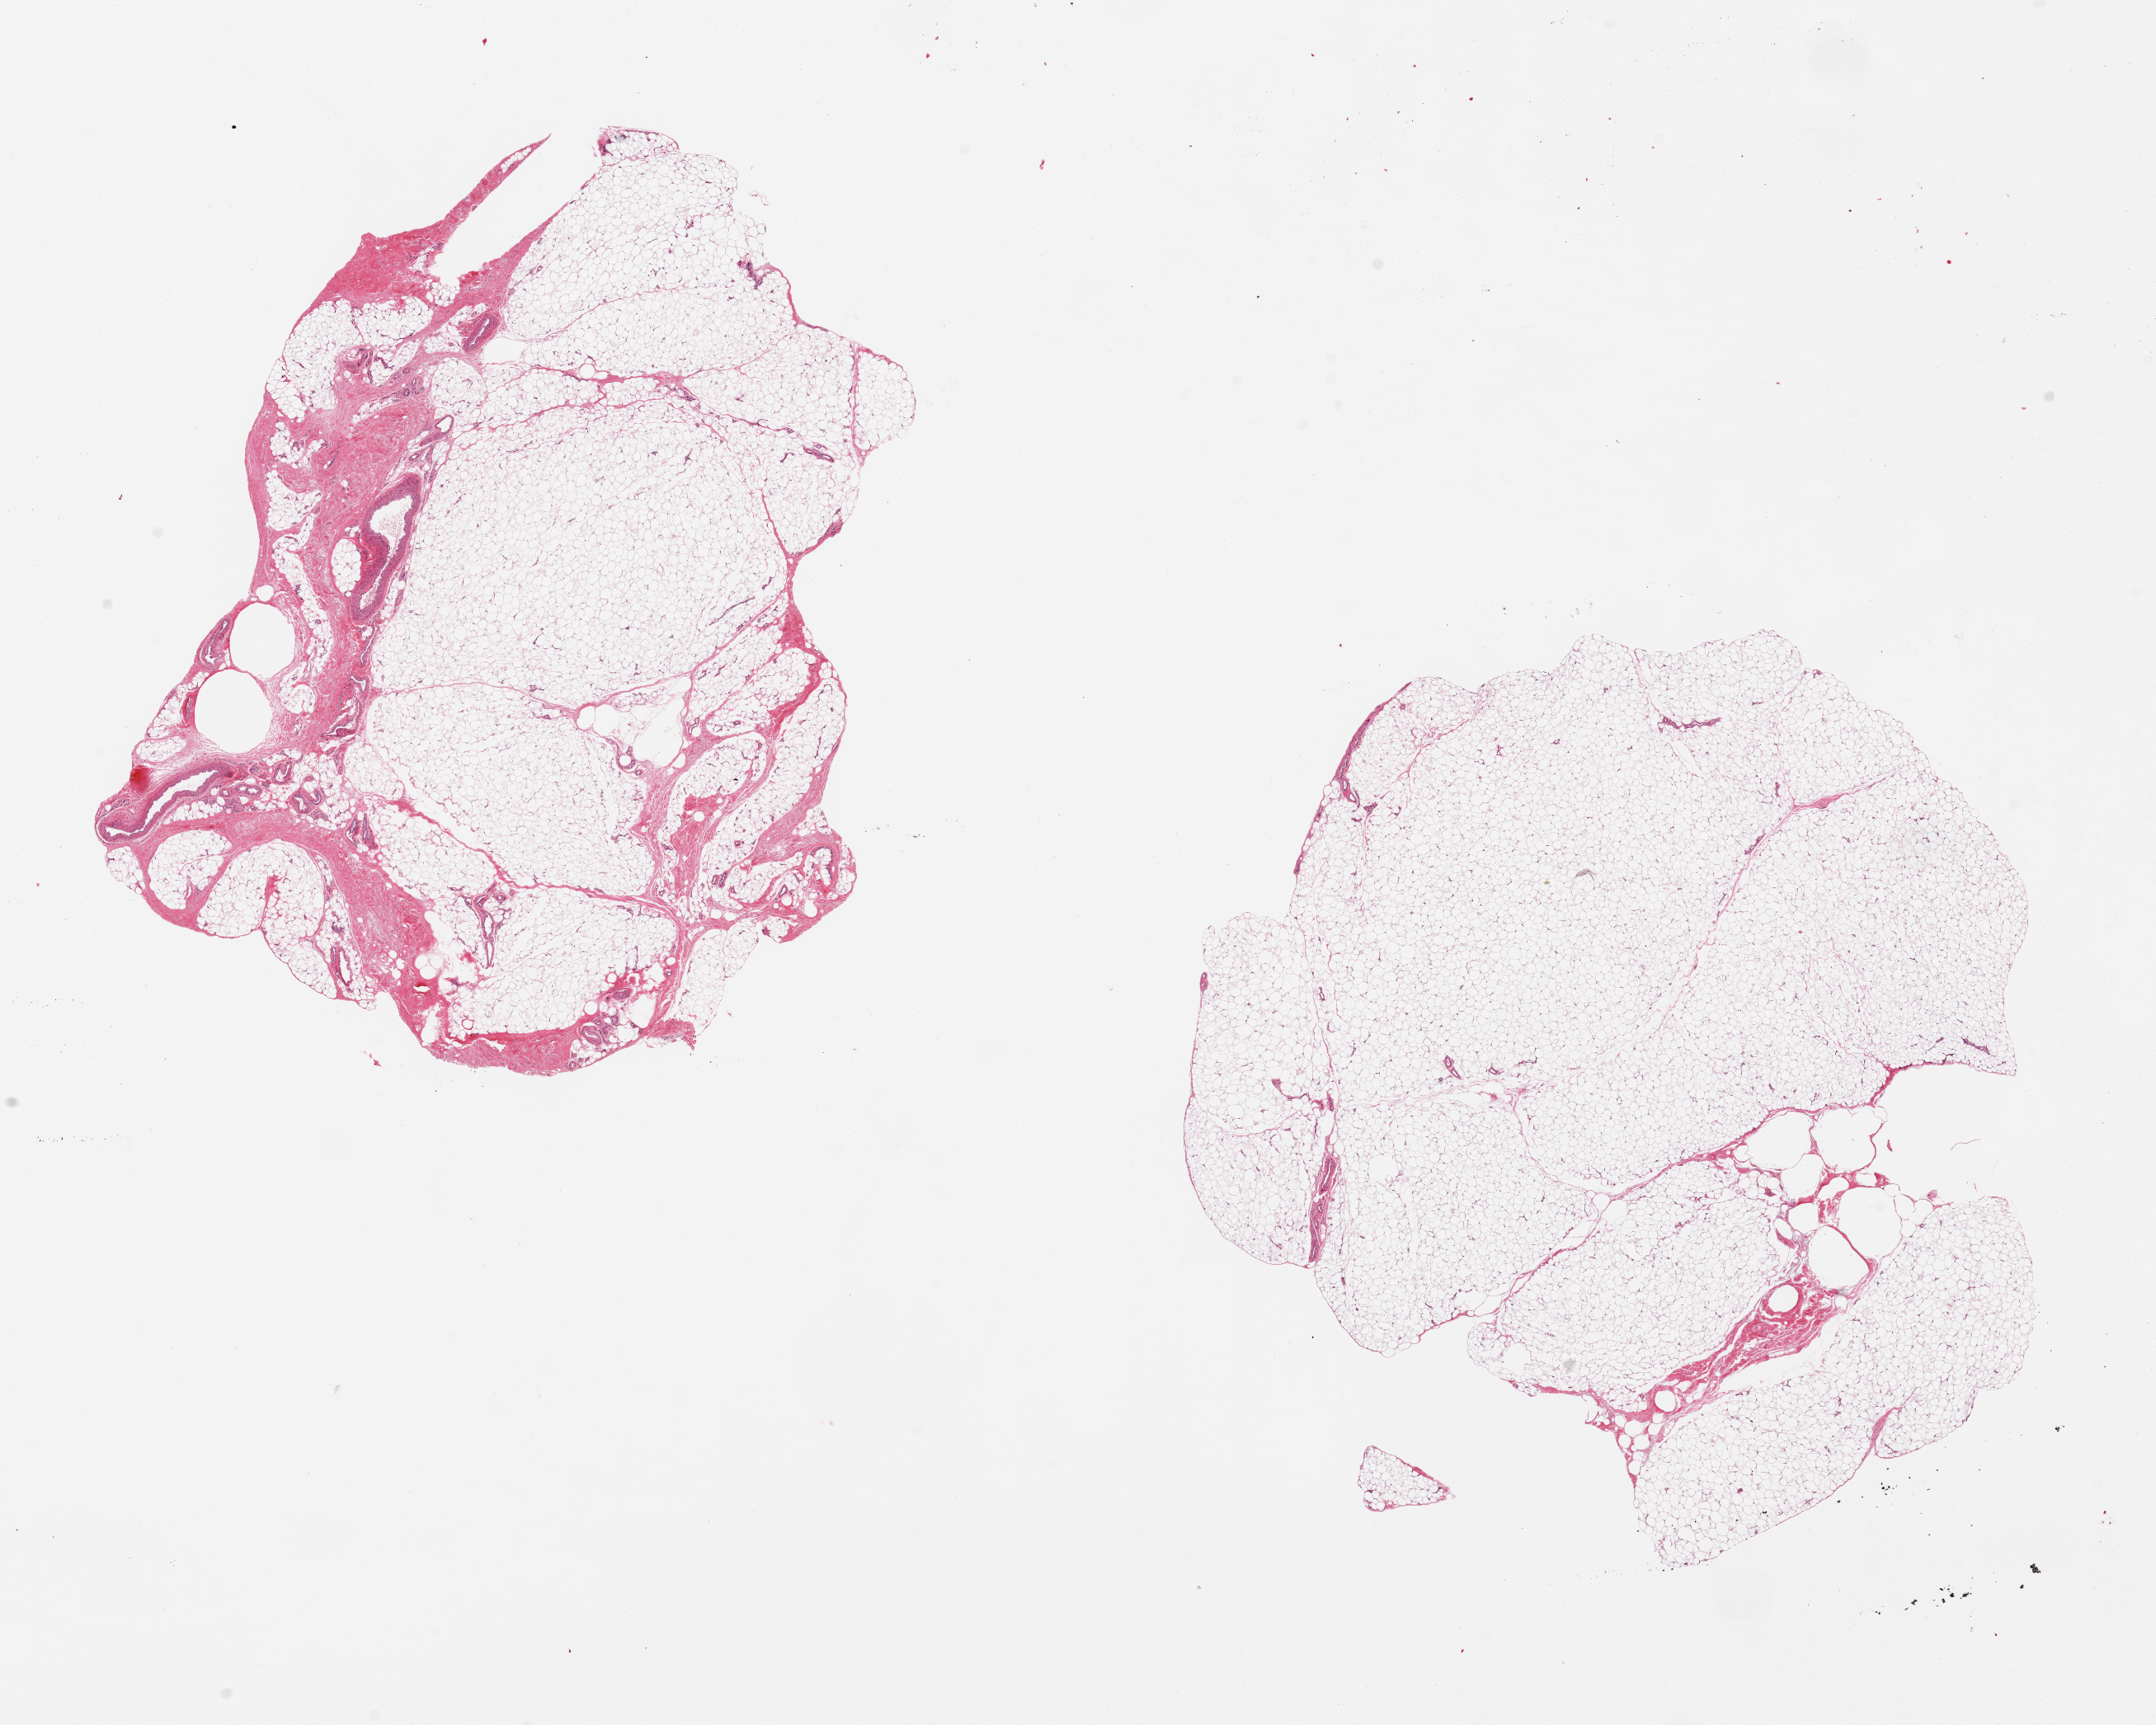
Digitized H&E-stained section, brightfield — shown as a low-resolution overview of the whole scanned area (about 20.7 x 16.5 mm, acquisition: 20x scan). PAXgene-fixed paraffin-embedded (PFPE) section. Target tissue: adipose tissue. Tissue donor sample. Male donor.
Pathologist's review note for this sample: 2 pieces; 9x7 & 9x8mm; ~10% fibrous components.